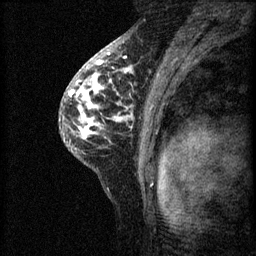
Breast MRI (dynamic contrast-enhanced), one sagittal slice; 3 images stored at this slice position (order not interpretable as contrast timing); 1.5 T; TE 4.2 ms, TR 8.2 ms; 2 mm slice thickness; 256 × 256 image matrix, field of view 180 × 180 mm. Patient: female, 41 years.
Structures marked on this image (semi-automatically segmented with operator editing):
- analysis volume of interest (the breast-tissue region the enhancement analysis was run in; not a lesion): bounding box [x1, y1, x2, y2] px = [59, 62, 159, 175]
- tumour enhancement mask (voxels above the 70 % enhancement threshold inside the analysis volume of interest): [68, 62, 152, 139]